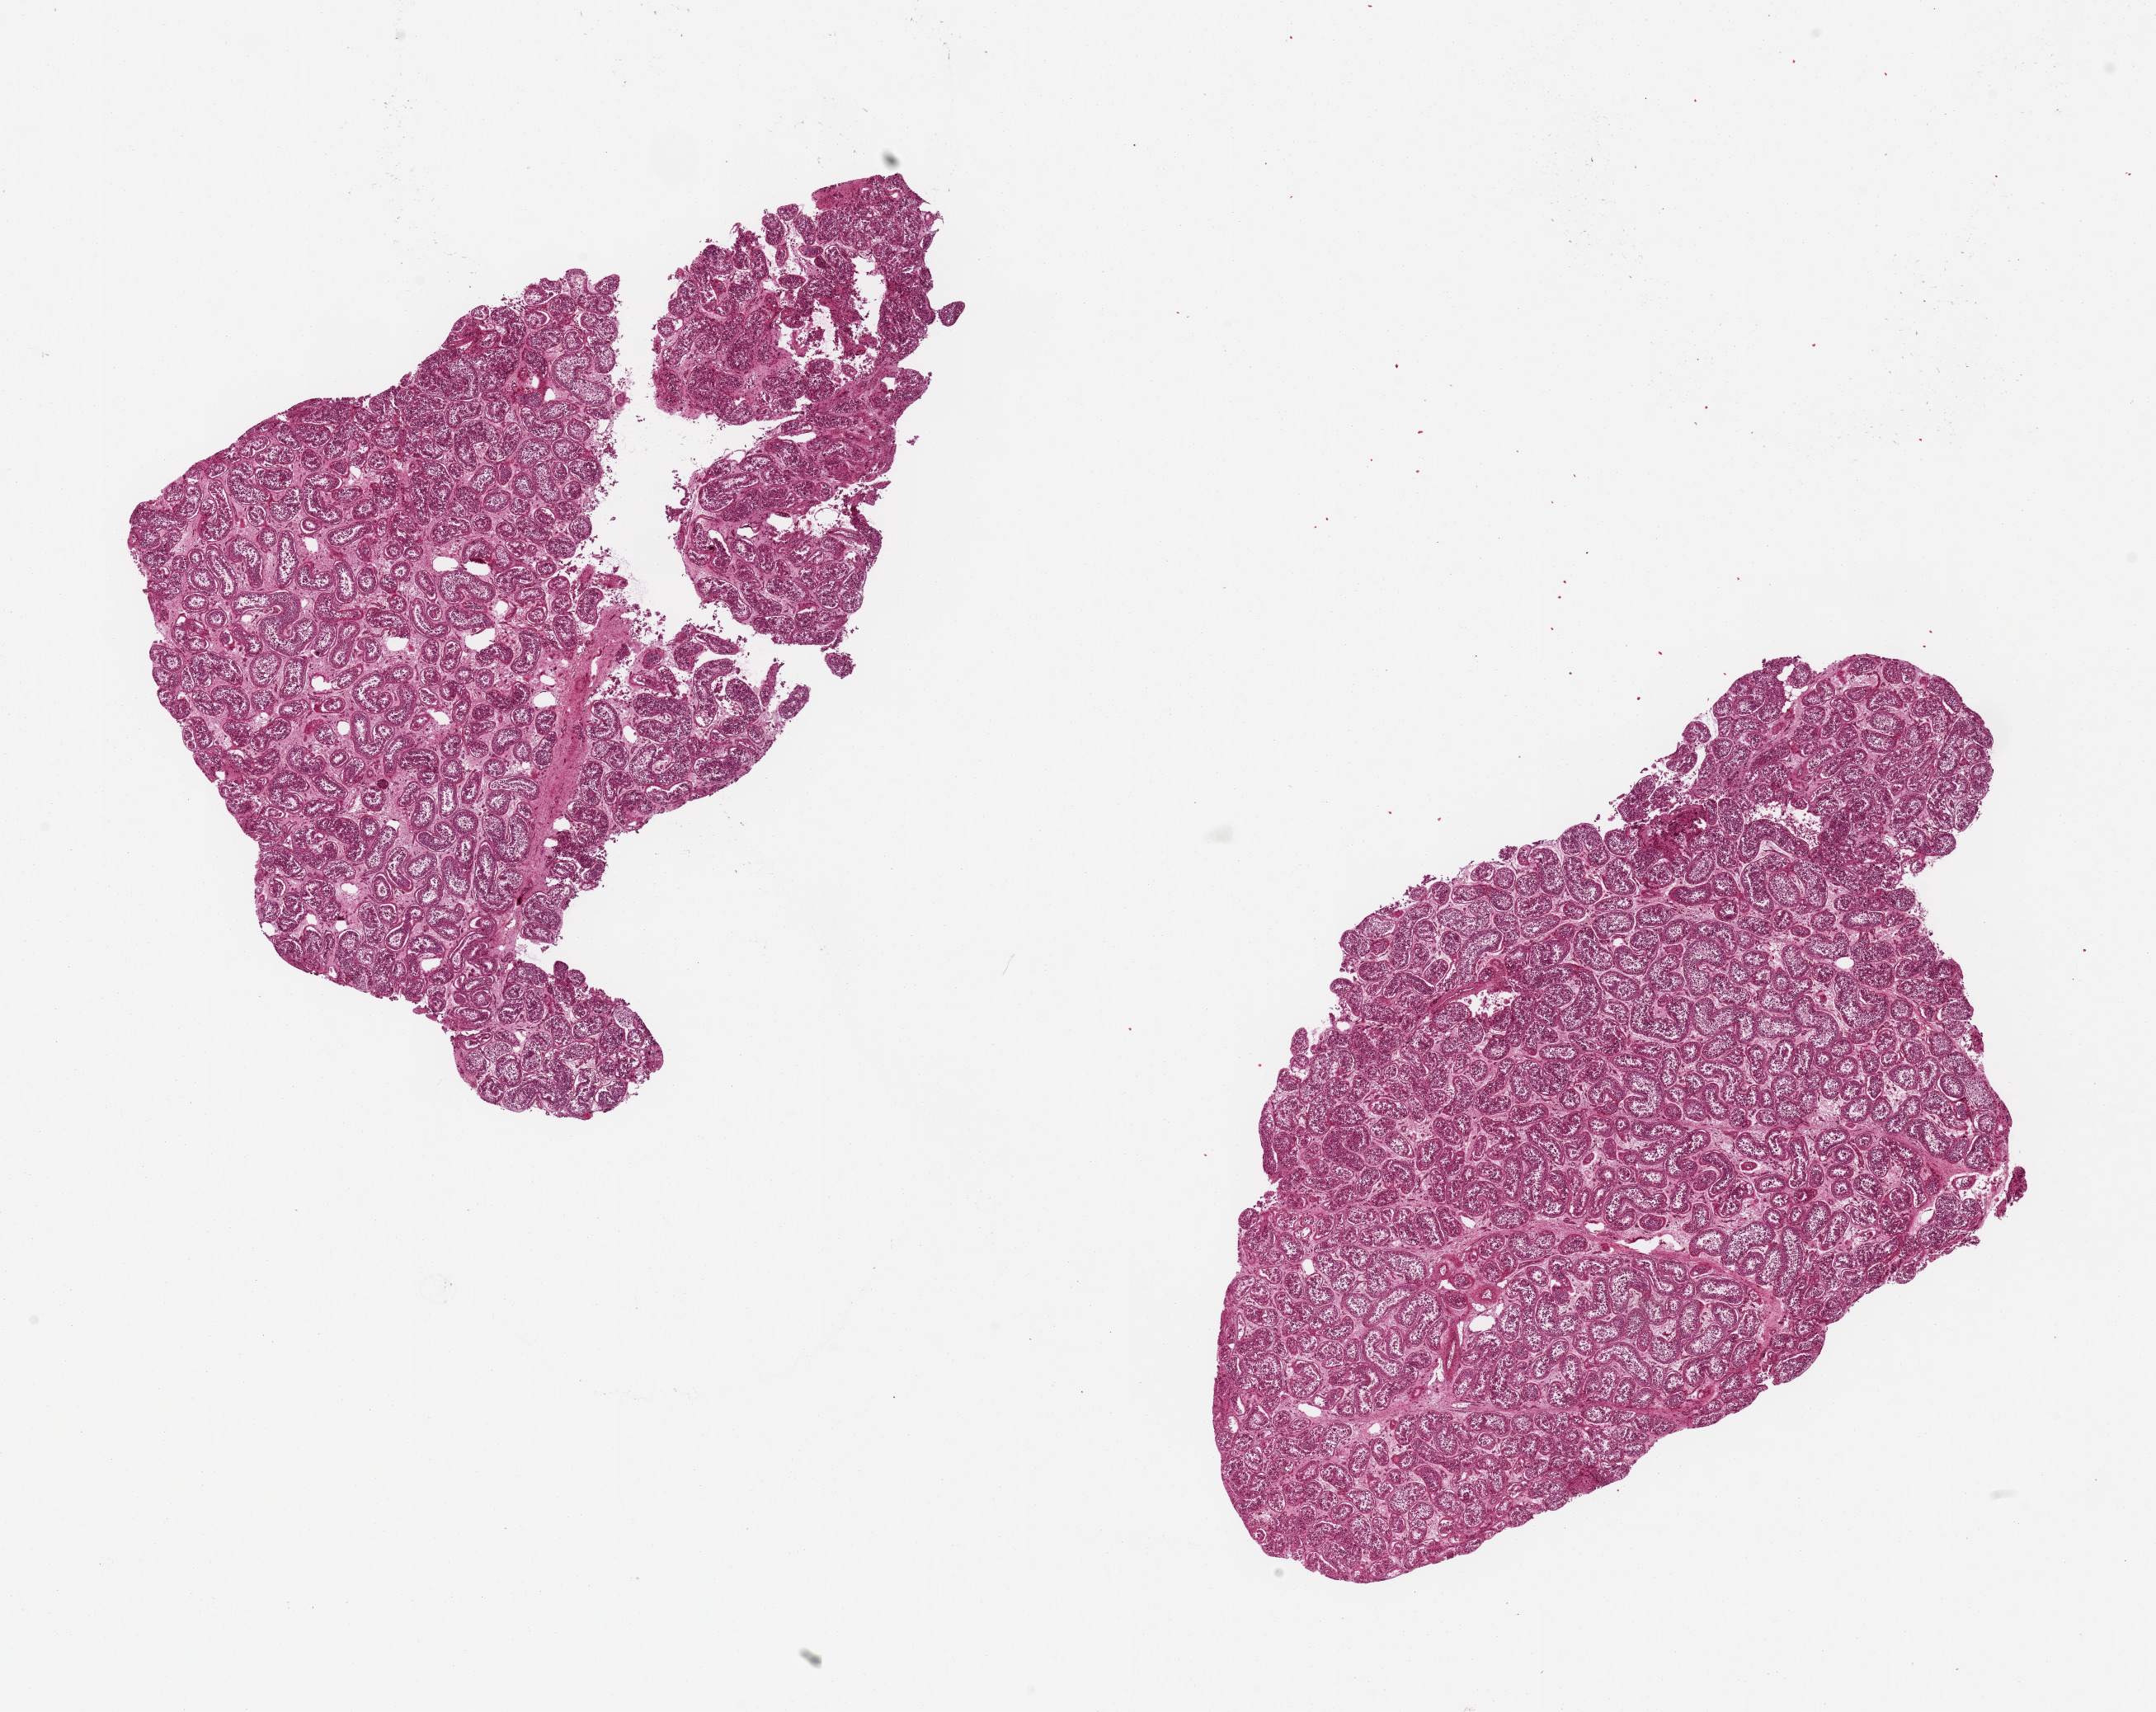
Digitized haematoxylin and eosin-stained section — whole scanned area (about 20.7 x 16.4 mm) shown as a low-resolution overview. PAXgene-fixed, paraffin-embedded tissue. Target tissue: testis. Donor tissue sample. Male donor.
Review note (as recorded): 2 pieces, 7x6 & 8x5 mm; spermatogenesis.